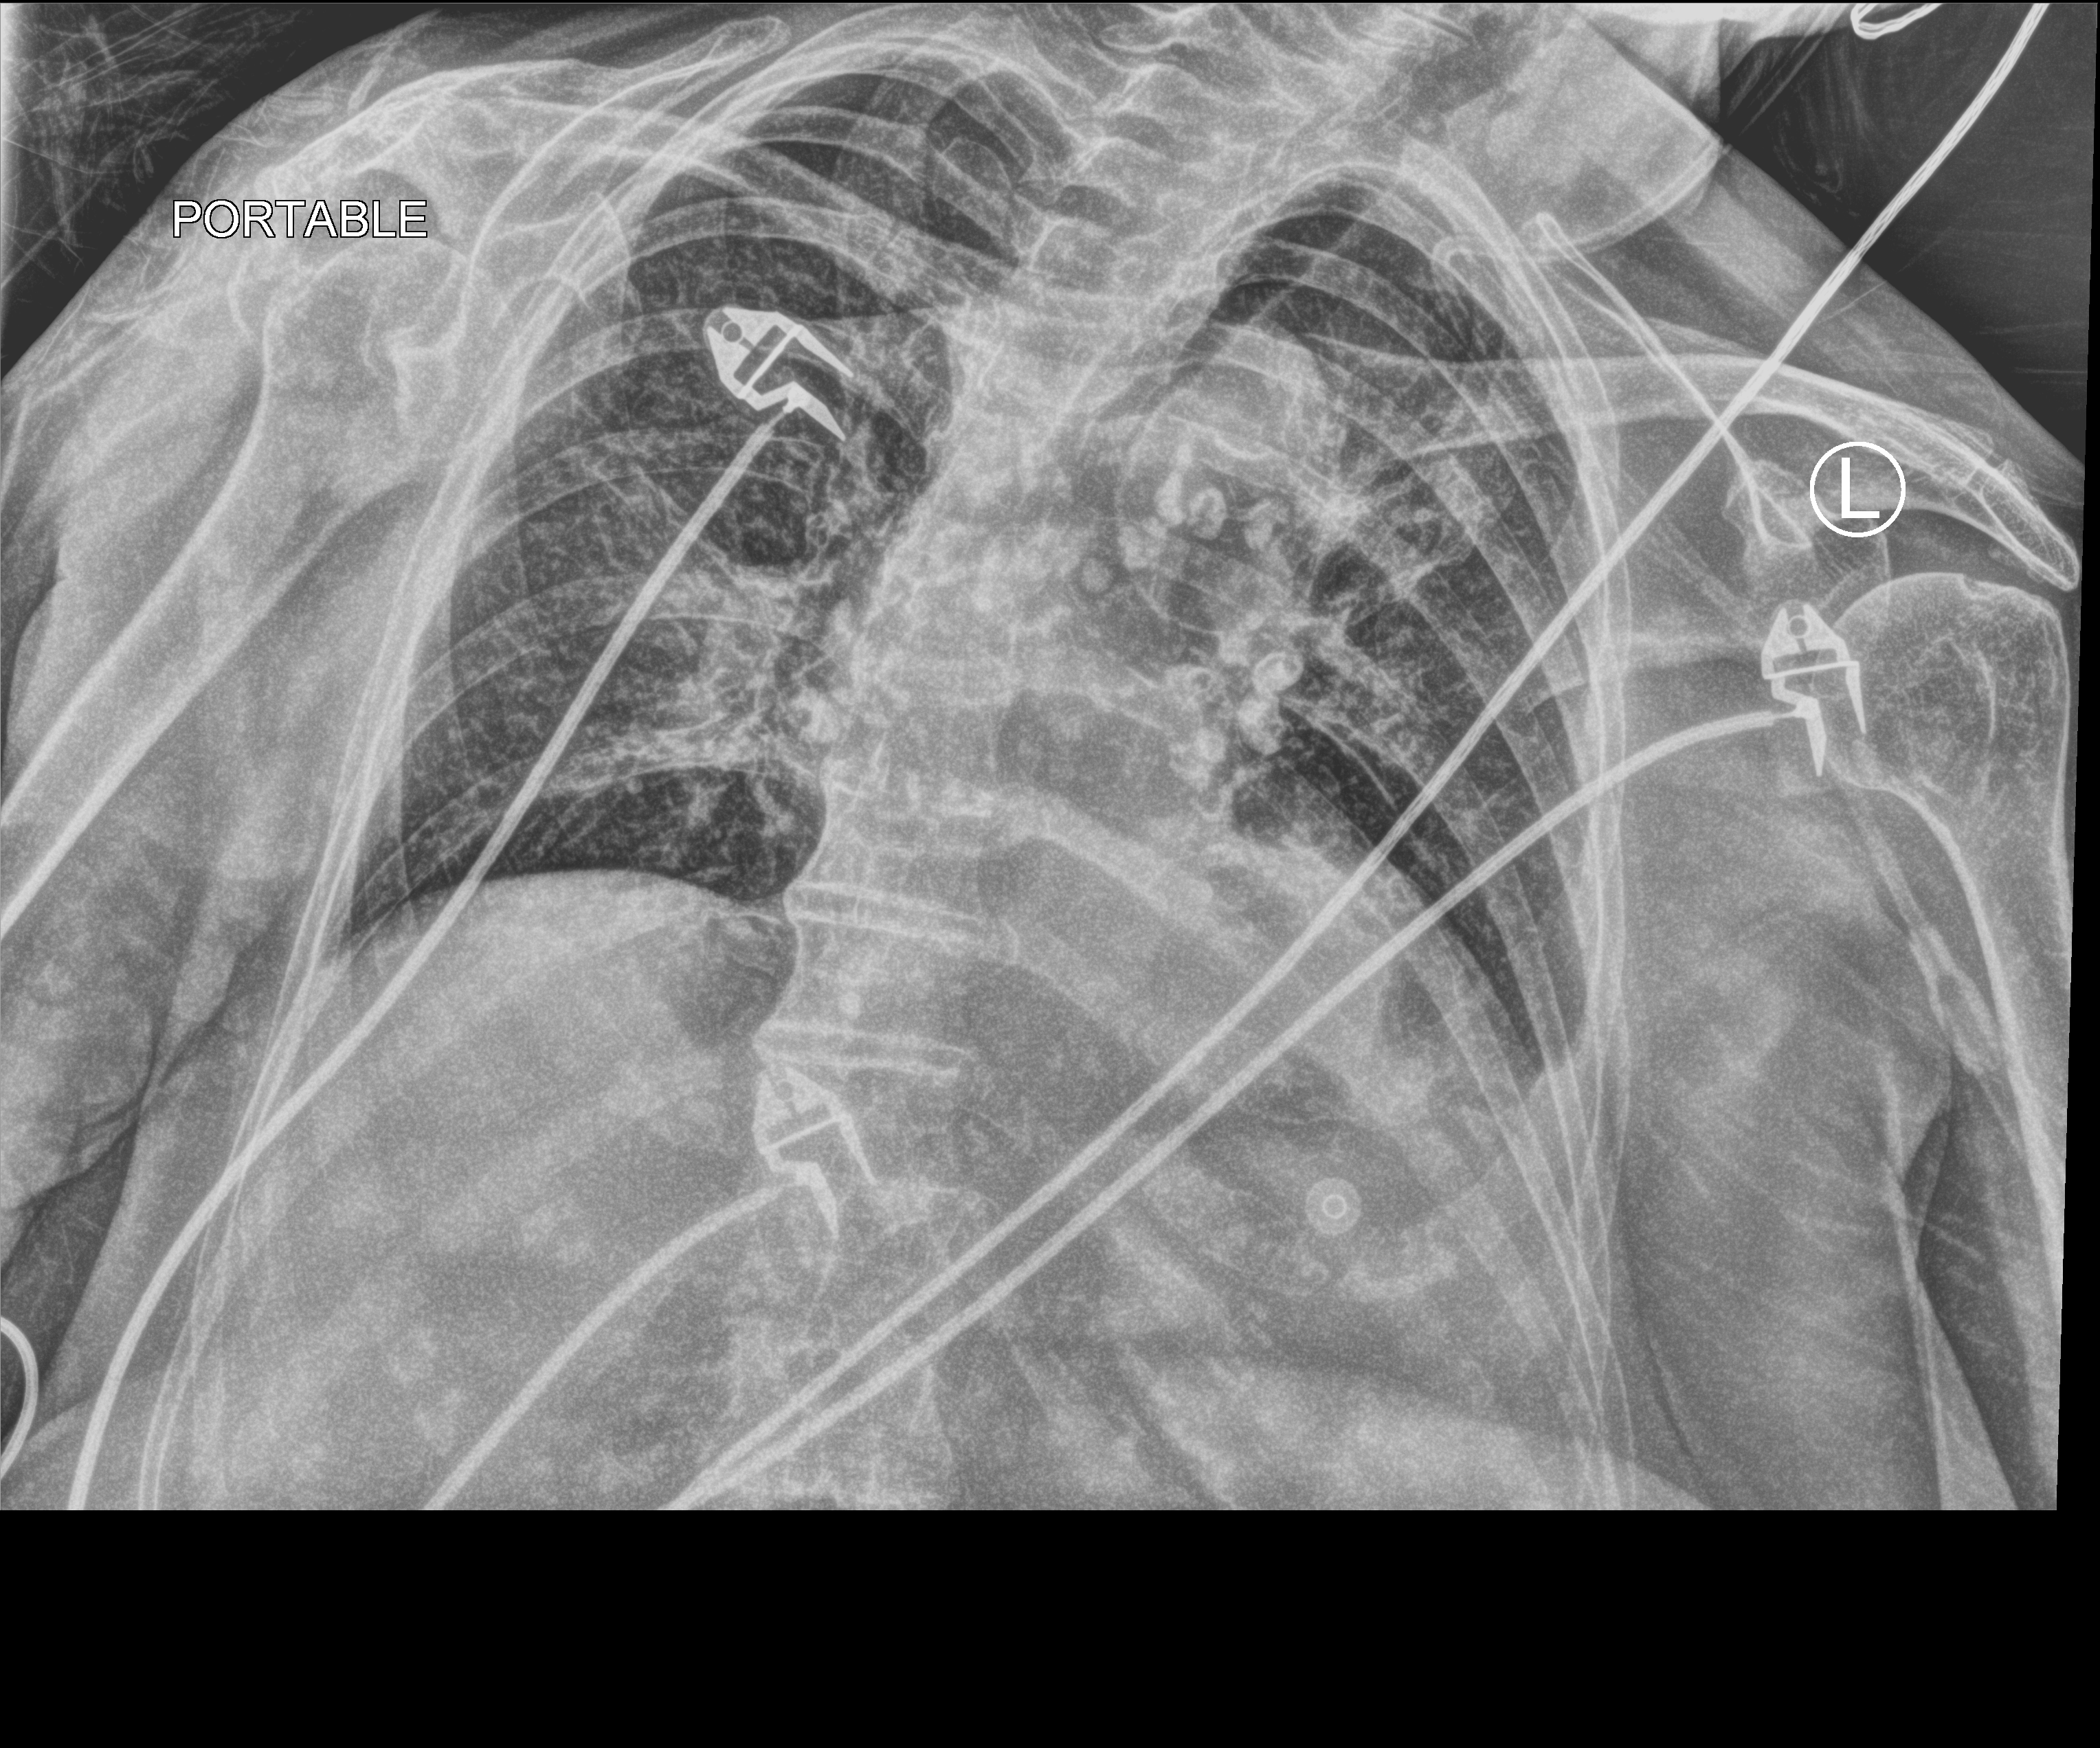
Chest X-ray (portable). Patient hospitalised with COVID-19; female, aged 75–90 years.
Hospital-stay facts (about this admission, not read from this image; timing relative to this image not recorded): mechanically ventilated during this hospital stay: no.